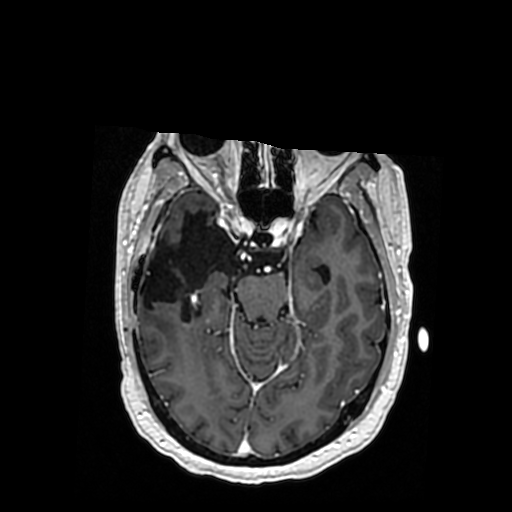
Brain MRI from a brain-tumour surgery series, one axial slice; slice 221 of 364 in the series (ordered by position); T1-weighted post-contrast; 512 × 512 image matrix. From the clinical record (not read from this slice): histopathology: Oligodendroglioma; WHO grade: 3; IDH mutation: yes.
Outlined on this slice (outlined manually by an expert reader):
- previous resection cavity: bounding box [x1, y1, x2, y2] px = [140, 211, 235, 320]